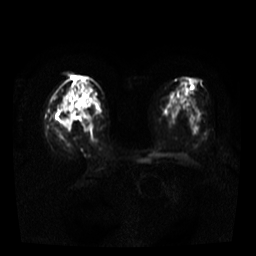
Breast MRI, one axial slice; slice 17 of 37 in the series (ordered by position); diffusion-weighted series; image 2 of 4 stored at this slice position (different b-values; order by instance number); 3 T; 5 mm slice thickness; 256 × 256 image matrix. Female patient.
Annotated regions visible in this slice (manually delineated by an expert):
- tumour on diffusion-weighted imaging: bounding box (x1, y1, x2, y2) in pixels: (61, 110, 77, 131)